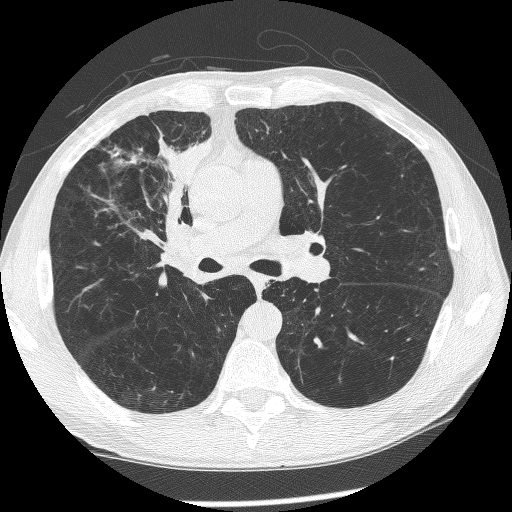
Chest CT (low-dose screening protocol), one axial image. Baseline screening round. Lung window (W 1500 / L -600 HU). Lung (sharp) reconstruction kernel (BONE). 512 × 512 image matrix, field of view 340 × 340 mm. Male participant, aged 60 years at enrolment.
Lesion marked by an expert reader, bounding box (x1, y1, x2, y2) in pixels: (145, 186, 218, 280). The exam's reader record, not a measurement of the box and not confirmed to be the same lesion: non-calcified nodule or mass ≥4 mm, right upper lobe, 12 × 8 mm, spiculated (stellate) margins, mixed attenuation. Later outcome: lung cancer diagnosed 208 days after this screen — squamous cell carcinoma, NOS, right upper lobe, right middle lobe, right main stem bronchus, poorly differentiated (G3), stage IV (AJCC 6th edition).